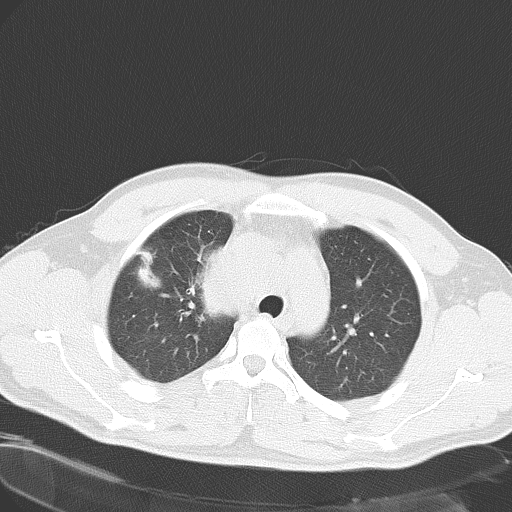
Chest CT, one axial slice. Position 42 of 55 along the scan axis. Reconstruction kernel B70f. Lung window (W 1500 / L -600 HU). 5 mm slice thickness. 512 × 512 image matrix, field of view 346 × 346 mm. Male patient, age 32 years. Case-level facts recorded for this patient, not image findings: clinical TNM (as recorded): T4 N3 M0; histopathological grade: G3.
Structures marked on this image (rectangle marked by the reading radiologist):
- lung tumour (recorded histology: small cell carcinoma): bounding box (x1, y1, x2, y2) in pixels: (193, 234, 243, 323)